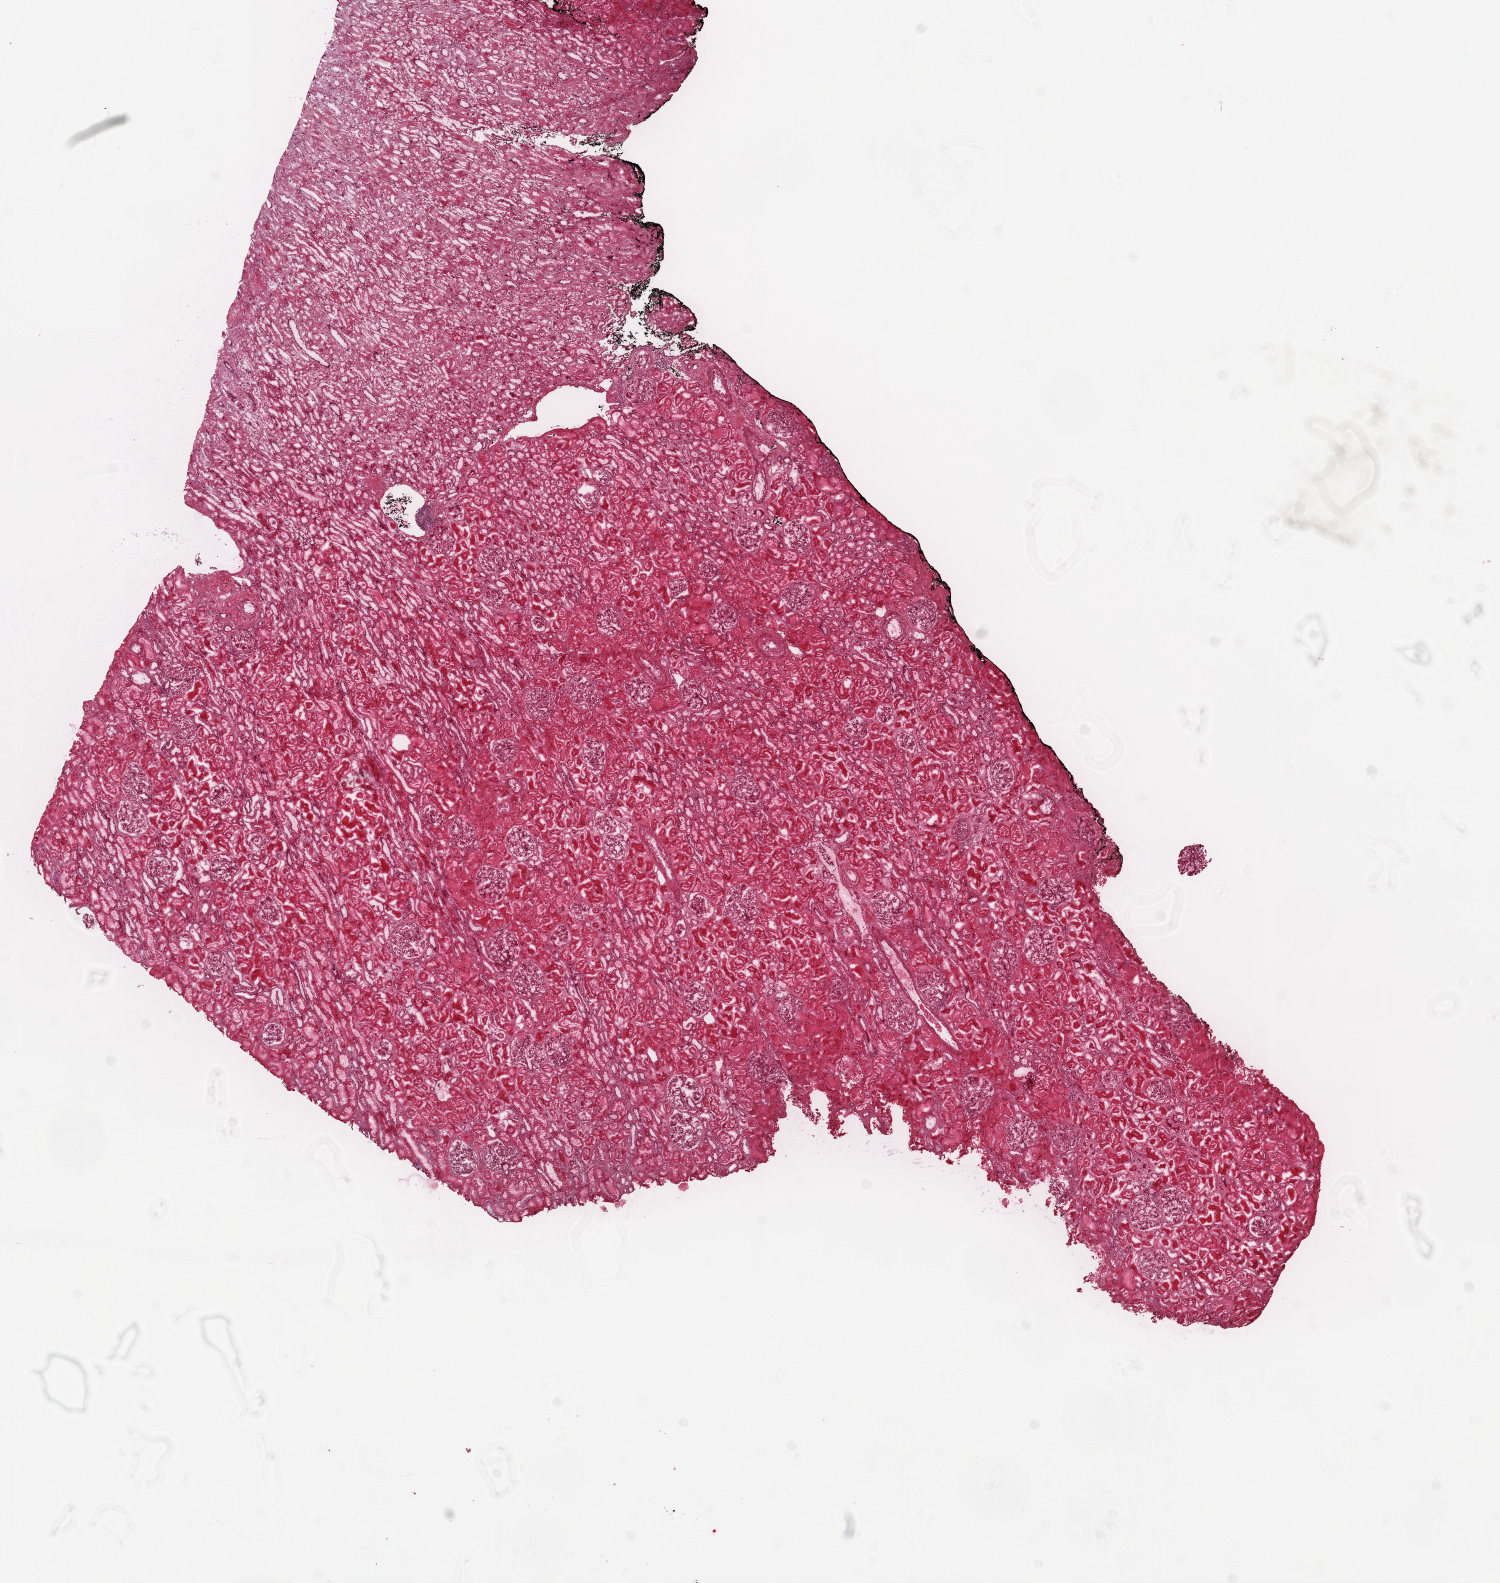
Digitized H&E-stained tissue section (whole slide), a low-resolution overview of the entire scanned area, about 12.0 x 12.7 mm; frozen section from the top of the tissue portion; kidney, solid tissue normal (non-tumour tissue) sample. Male, age 46 years at initial diagnosis.
* this section: solid tissue normal sample (biorepository sample class)
* patient diagnosis: Clear cell adenocarcinoma, NOS